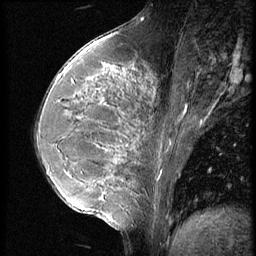
Breast MRI (dynamic contrast-enhanced), one sagittal slice. Slice 23 of 56 in the series (ordered by position). 3 images stored at this slice position (order not interpretable as contrast timing). 1.5 T. TE 4.2 ms, TR 9 ms. 2.5 mm slice thickness. 256 × 256 image matrix, field of view 180 × 180 mm. Female patient, age 35 years. Case-level facts recorded for this patient, not image findings: setting: breast cancer imaged before/during neoadjuvant chemotherapy; receptor status: HR-positive, HER2-negative.
Structures marked on this image (semi-automatically segmented with operator editing):
- analysis volume of interest (the breast-tissue region the enhancement analysis was run in; not a lesion): bounding box <63,60,175,218> (left, top, right, bottom; pixels)
- tumour enhancement mask (voxels above the 140 % enhancement threshold inside the analysis volume of interest): <89,66,127,187>